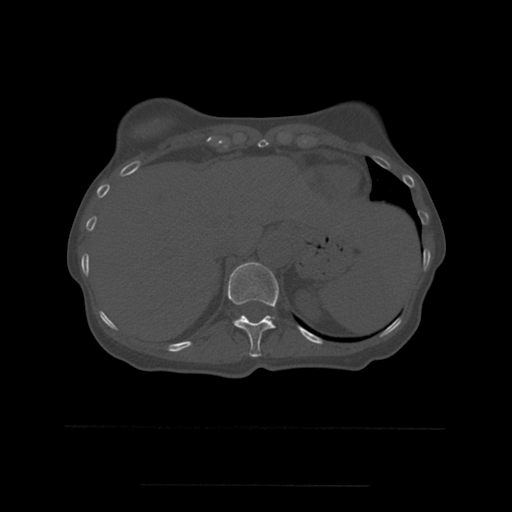
CT including the spine, one axial slice. Slice 277 of 544 in the series (ordered by position). Bone window (W 1800 / L 400 HU). 1.25 mm slice thickness. 512 × 512 image matrix. Patient age 58 years. Case-level facts recorded for this patient, not image findings: primary cancer: lung.
Outlined on this slice (semi-automatic segmentation, software-assisted and operator-edited):
- T11 vertebra: bounding box <228,262,279,358> (left, top, right, bottom; pixels)